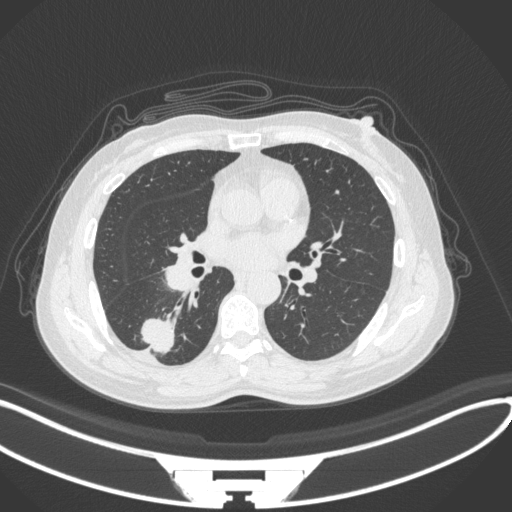
Chest CT, one axial slice; position 154 of 352 along the scan axis; lung window (W 1500 / L -600 HU); 512 × 512 image matrix, field of view 400 × 400 mm. Patient: female, 55 years. From the clinical record (not read from this slice): clinical TNM (as recorded): T1c N1 M0.
Outlined on this slice (rectangle marked by the reading radiologist):
- lung tumour (recorded histology: adenocarcinoma): bounding box [x1, y1, x2, y2] px = [135, 317, 180, 356]